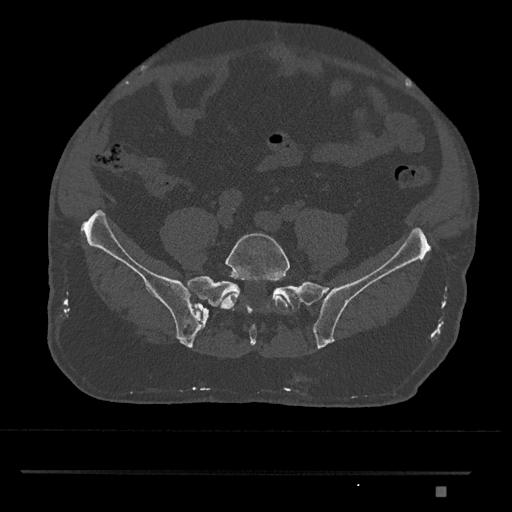
CT including the spine, one axial slice; slice 533 of 1134 in the series (ordered by position); 120 kVp; bone window (W 1800 / L 400 HU); 512 × 512 image matrix, field of view 429 × 429 mm. Male patient, age 65 years. Case-level facts recorded for this patient, not image findings: primary cancer: prostate.
Annotated regions visible in this slice (semi-automatically segmented with operator editing):
- L5 vertebra: box from (x=220, y=233) to (x=290, y=313) px